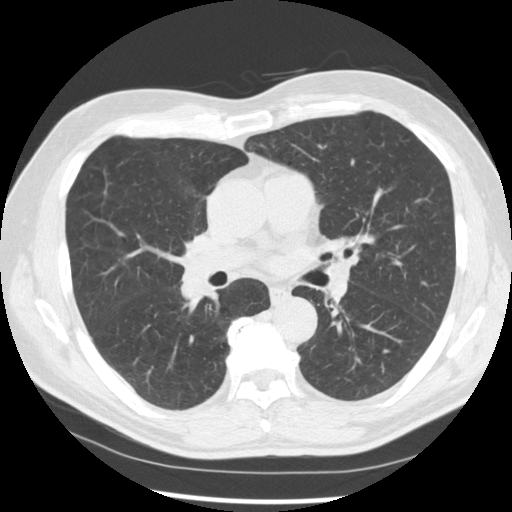
Axial slice from a low-dose chest CT screening exam. Baseline screening round. Lung window (W 1500 / L -600 HU). 2.5 mm slice thickness. Slice 156 of 277 in the series. Male participant, aged 67 years at enrolment.
Expert reader's lesion annotation, bounding box (x1, y1, x2, y2) in pixels: (161, 248, 229, 311). The exam's reader record, not a measurement of the box and not confirmed to be the same lesion: non-calcified nodule or mass ≥4 mm, left lower lobe, 15 × 15 mm, spiculated (stellate) margins, soft tissue attenuation. Note: the box lies in the patient's right hemithorax on this image, whereas the reader's record names the left lung; they may be different findings. Official screen result: positive, change unspecified: nodule(s) >= 4 mm or enlarging nodule(s), mass(es), or other non-specific abnormalities suspicious for lung cancer. Lung cancer was diagnosed 49 days after this screen: squamous cell carcinoma, NOS, right middle lobe, poorly differentiated (G3), stage IIB (AJCC 6th edition), 35 mm at pathology.